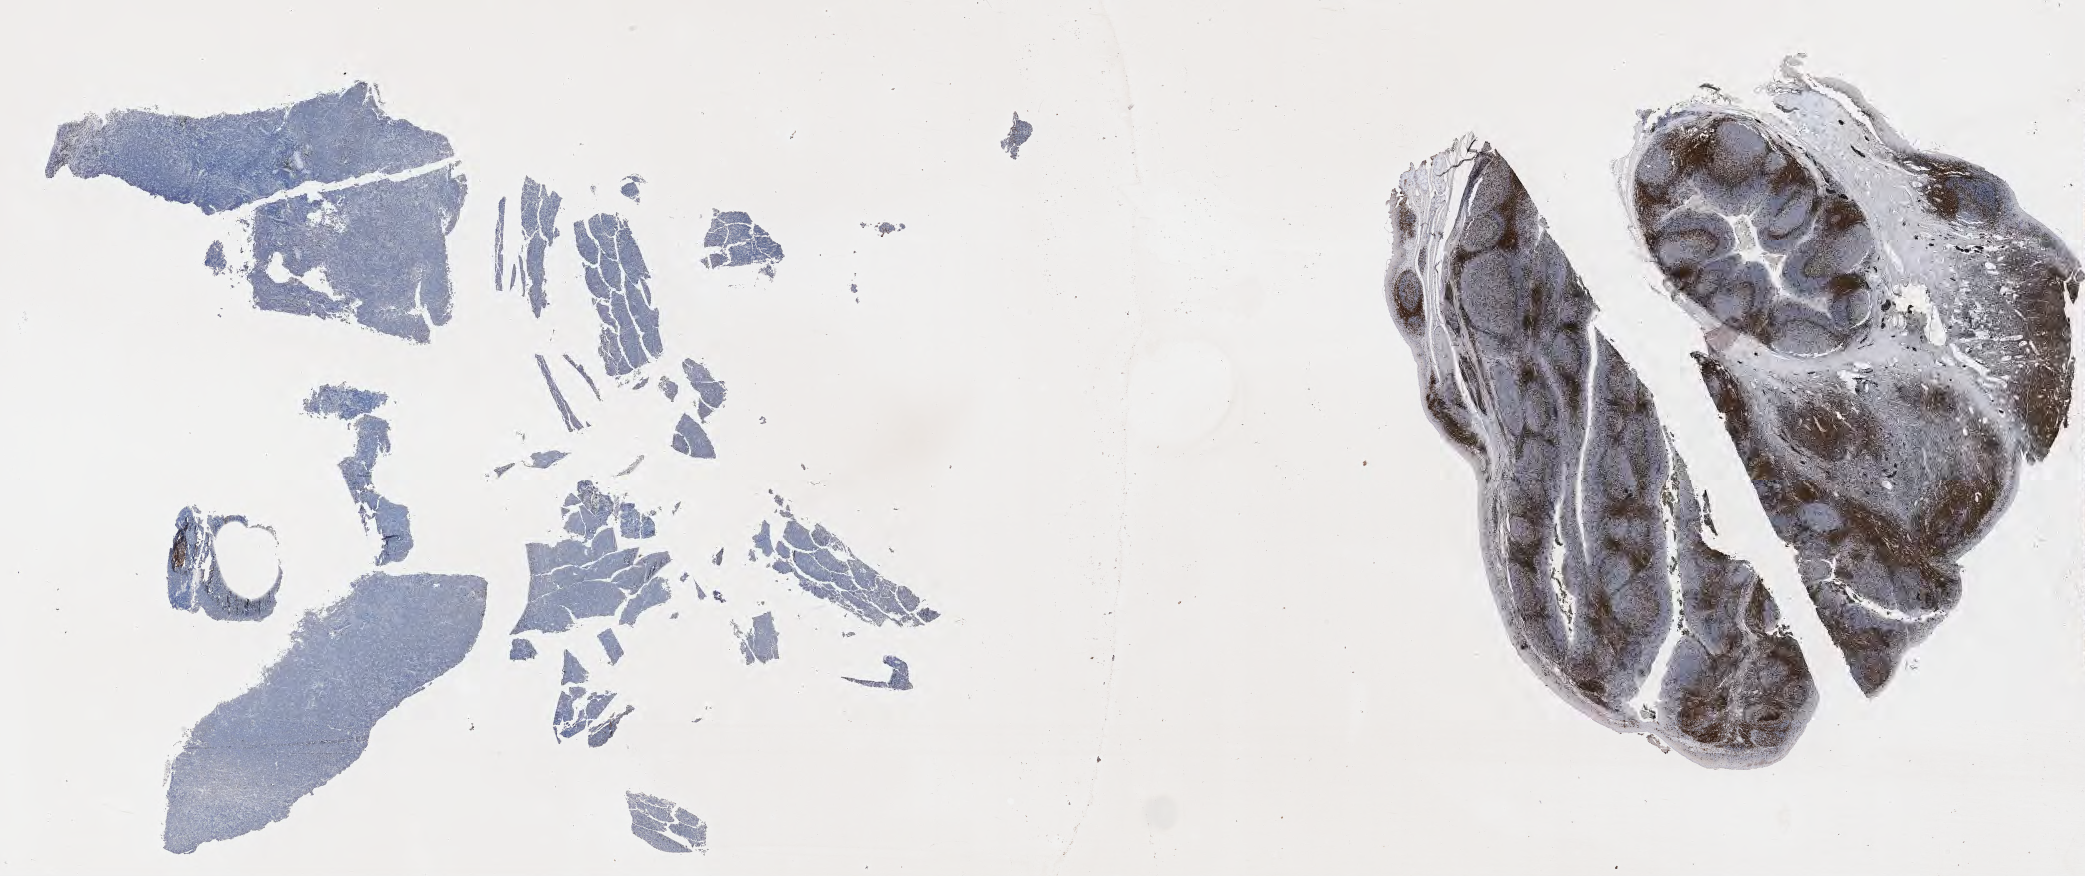
Whole-slide image, immunohistochemical stain for CD3 — a low-resolution overview of the entire scanned area, about 33.7 x 14.2 mm. Tumor tissue. Male, age 9 years at initial diagnosis.
• histologic diagnosis: Burkitt lymphoma, NOS